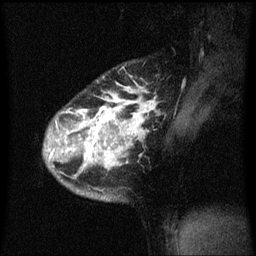
Breast MRI (dynamic contrast-enhanced), one sagittal slice; position 49 of 60 along the scan axis; dynamic contrast-enhanced series, image 2 of 3 at this slice position (ordered by acquisition); 1.5 T; TE 4.2 ms, TR 8.4 ms; 2 mm slice thickness; 256 × 256 image matrix, field of view 200 × 200 mm. Female patient, age 34 years. From the clinical record (not read from this slice): setting: breast cancer imaged before/during neoadjuvant chemotherapy; receptor status: HR-positive, HER2-negative.
Annotated regions visible in this slice (semi-automatically segmented with operator editing):
- analysis volume of interest (the breast-tissue region the enhancement analysis was run in; not a lesion): bounding box (x1, y1, x2, y2) in pixels: (44, 60, 163, 203)
- tumour enhancement mask (voxels above the 70 % enhancement threshold inside the analysis volume of interest): (50, 86, 157, 167)